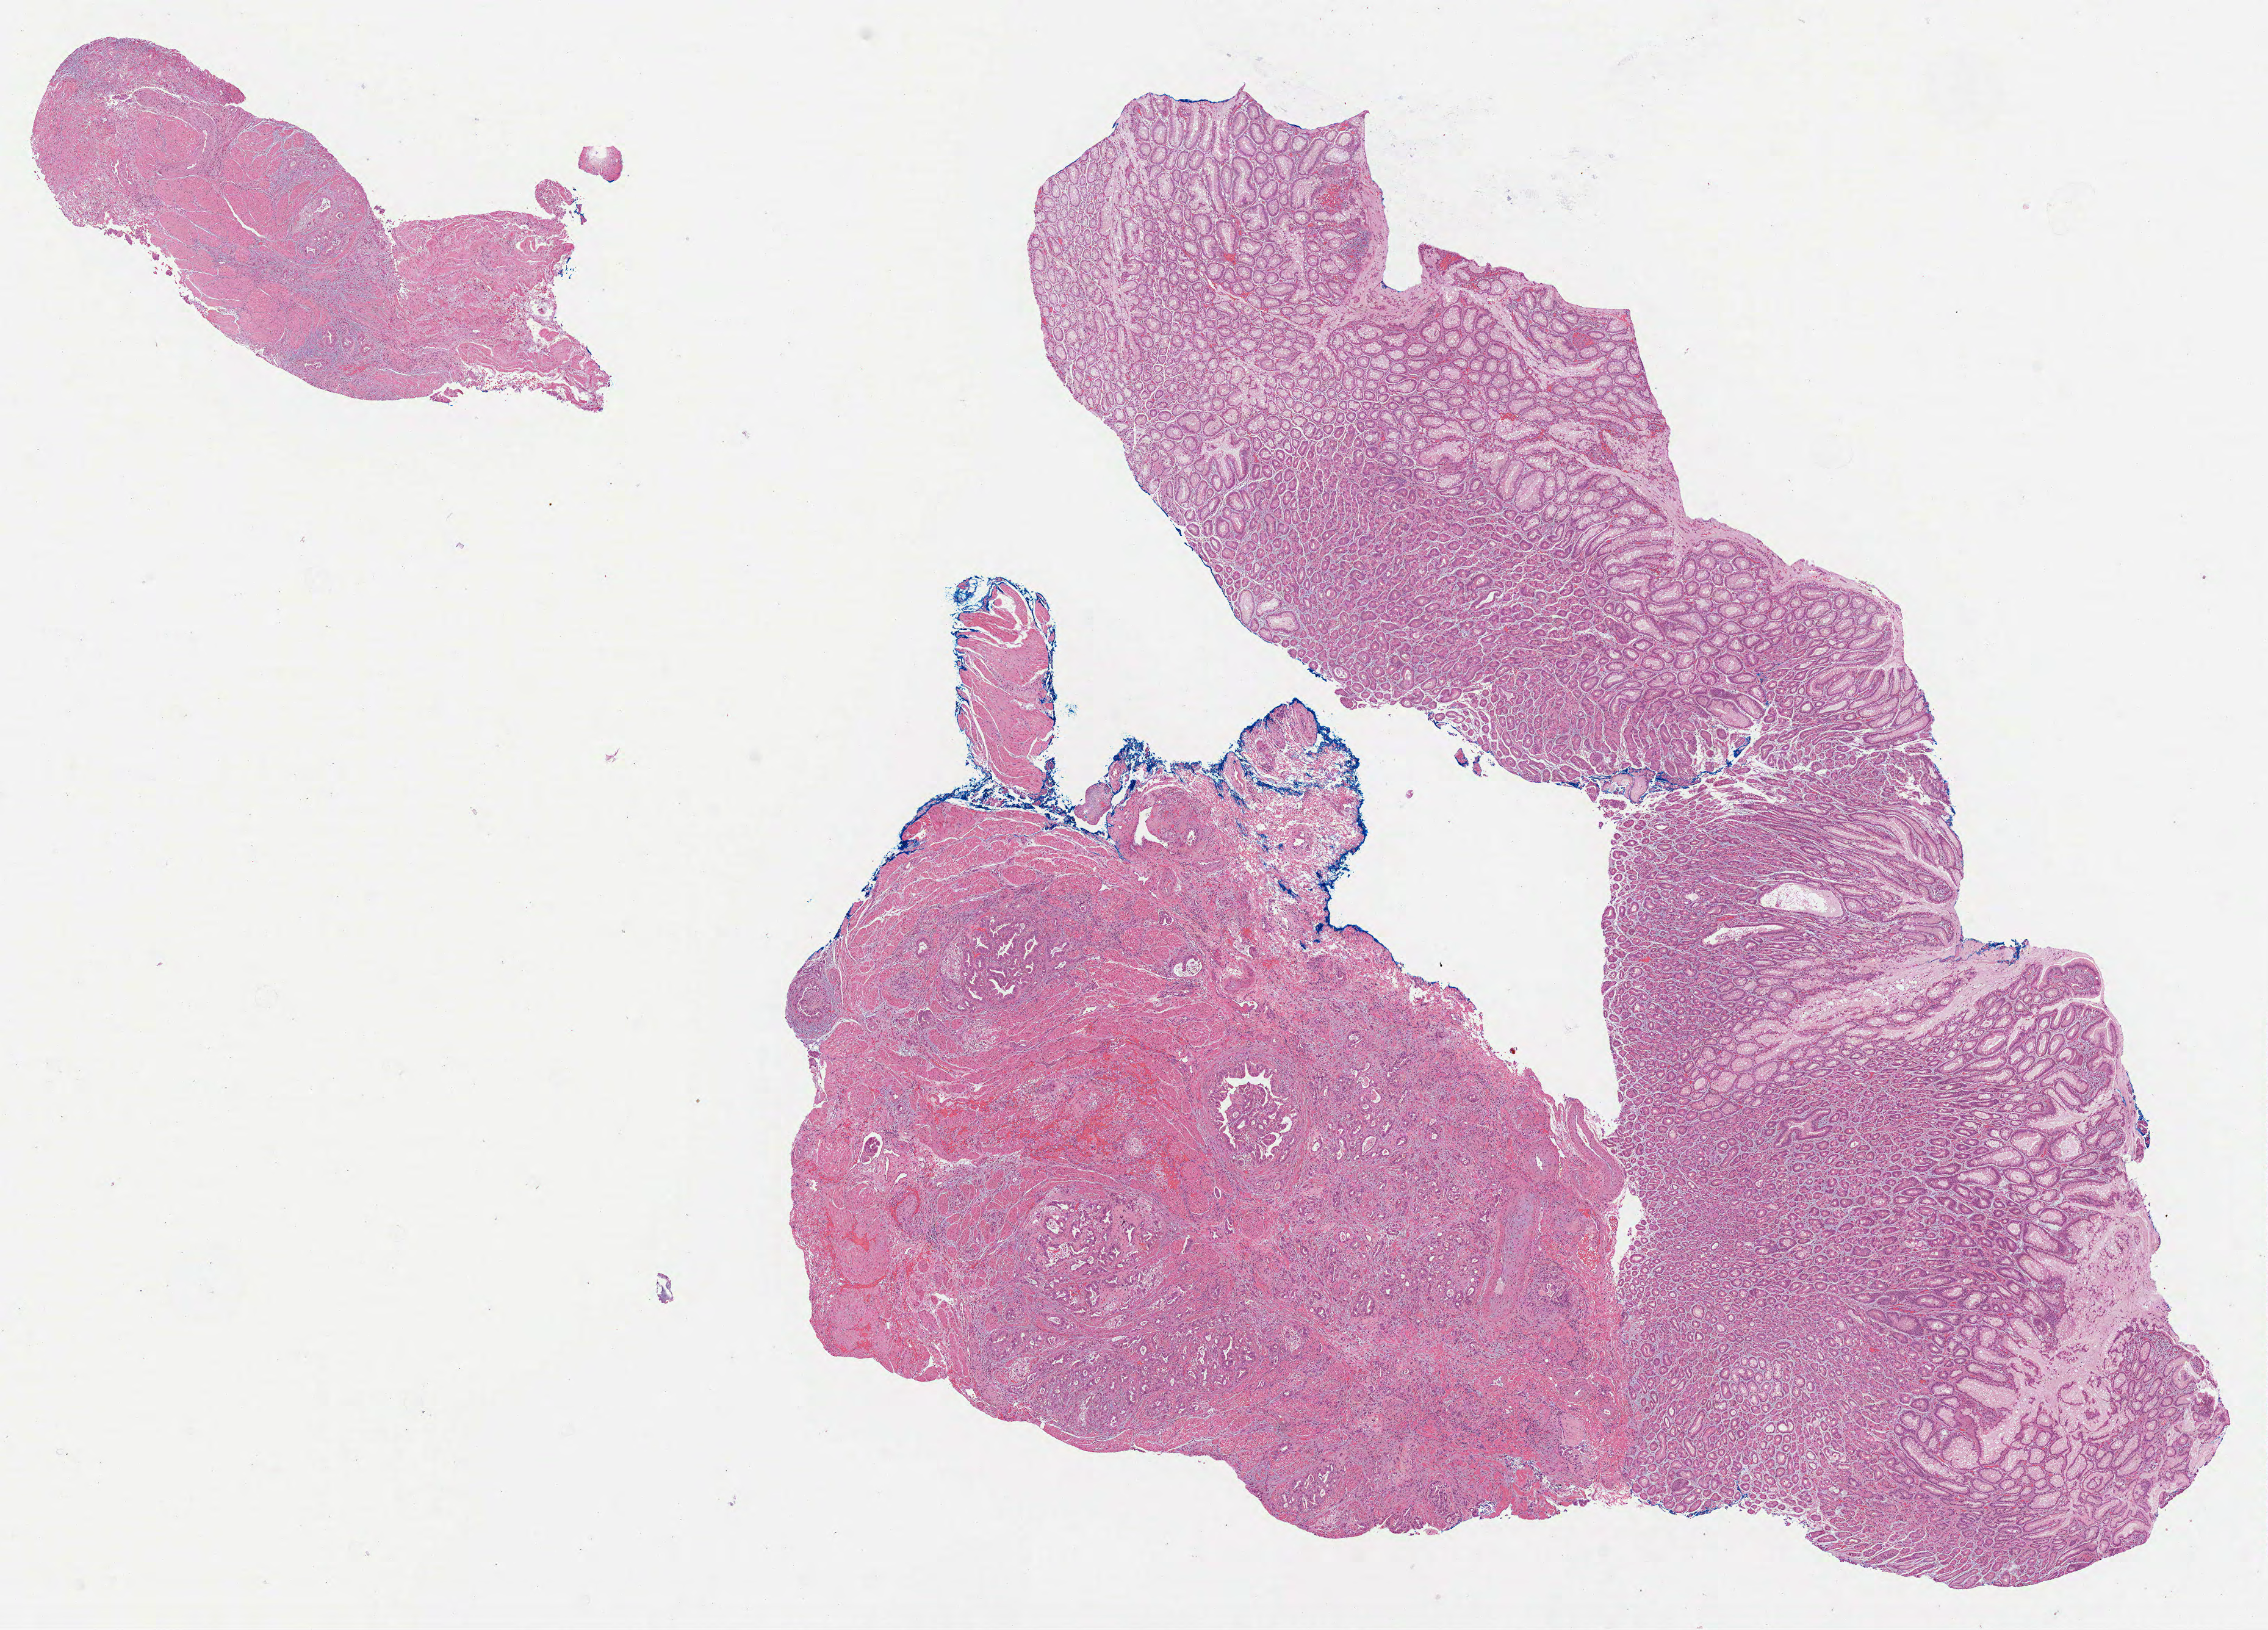
H&E whole-slide image, whole scanned area (about 15.0 x 10.8 mm) shown as a low-resolution overview; formalin-fixed paraffin-embedded (FFPE) diagnostic section; primary tumour sample from the stomach. Male, age 68 years at initial diagnosis. Histologic grade: G2 (moderately differentiated).
TNM: T3 N2 MX. Histologic diagnosis: Adenocarcinoma, intestinal type (cardia, NOS). AJCC pathologic stage: IIIA (7th edition).